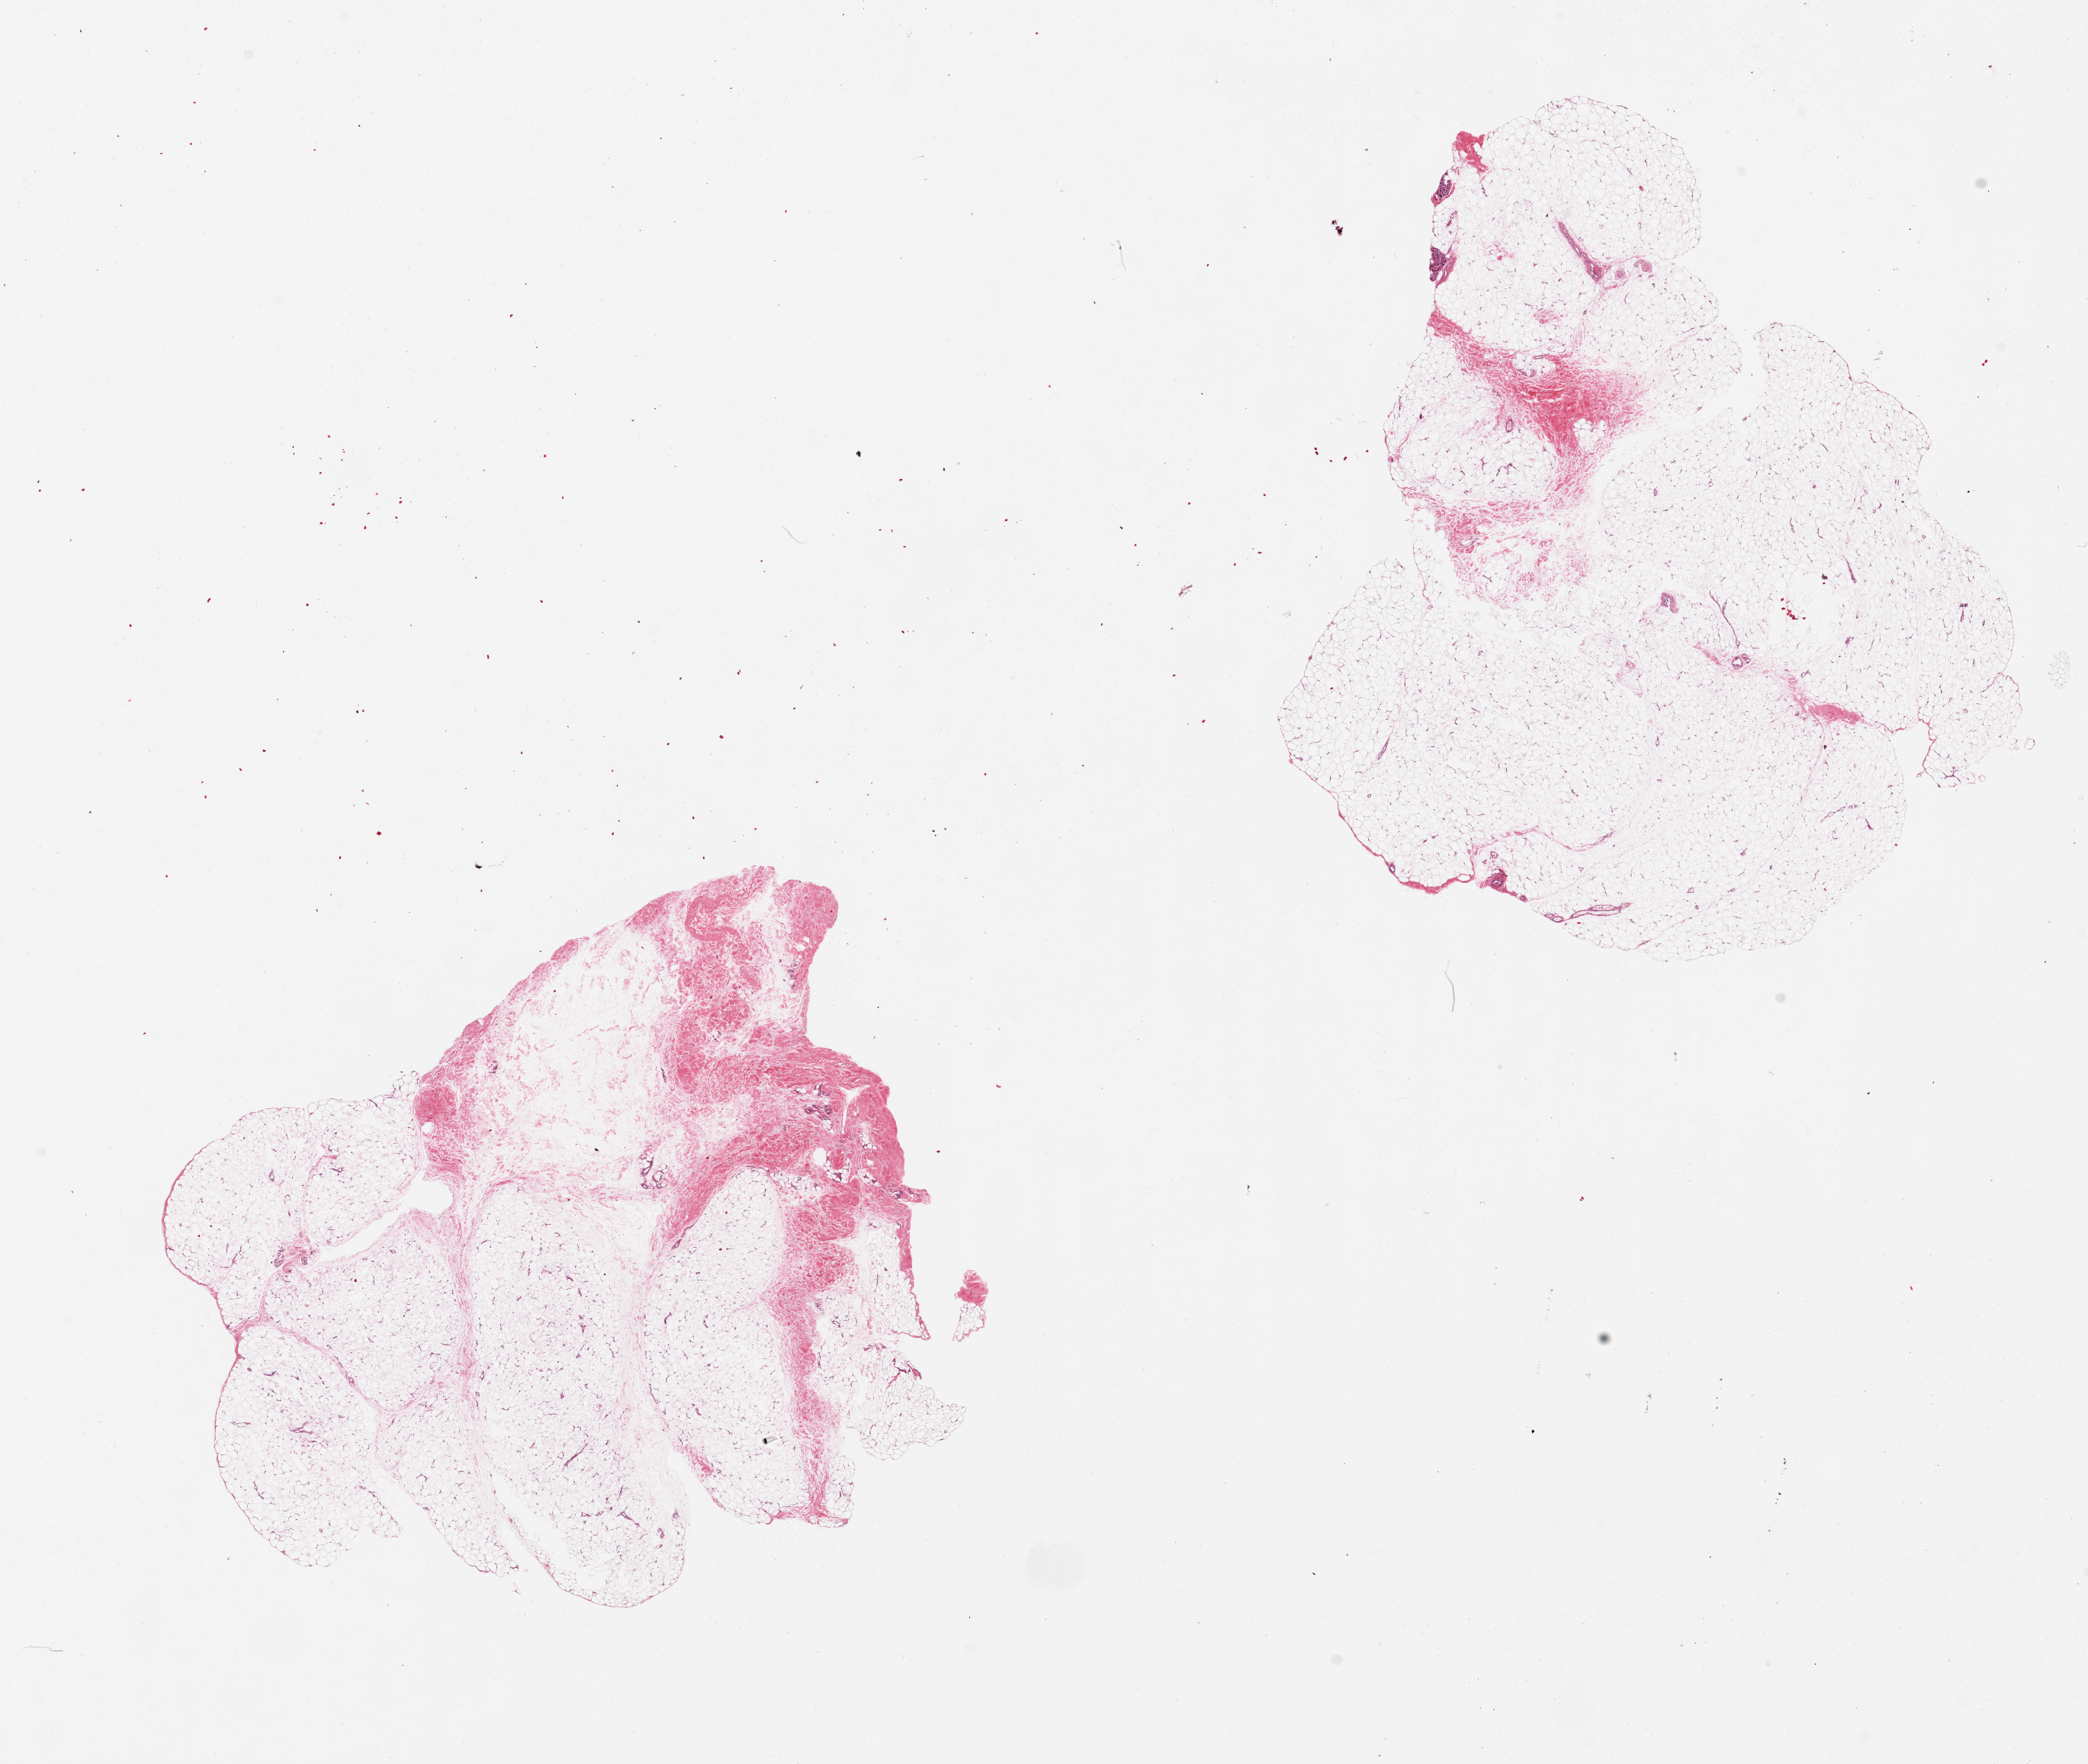
Whole-slide image, H&E stain, a low-resolution overview of the entire scanned area, about 21.7 x 18.3 mm (acquisition: 20x scan); PAXgene-fixed, paraffin-embedded tissue; section of adipose tissue (target tissue); tissue donor sample.
Review note (as recorded): 2 pieces, some fibrous stroma and few sweat glands.